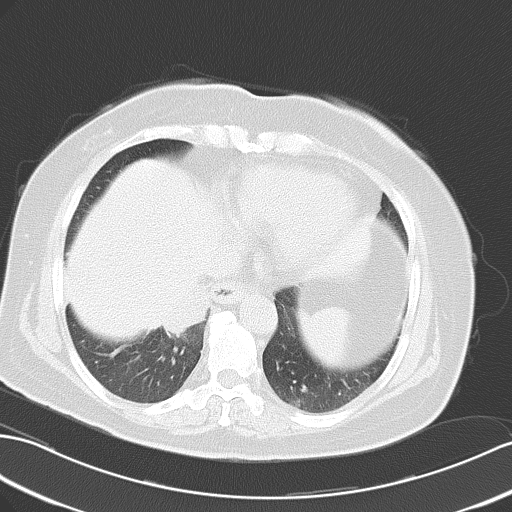
Chest CT, one axial slice. Position 16 of 50 along the scan axis. Reconstruction kernel B70f. 120 kVp. Lung window (W 1500 / L -600 HU). 5 mm slice thickness. 512 × 512 image matrix, field of view 353 × 353 mm. Female patient, age 63 years. From the clinical record (not read from this slice): clinical TNM (as recorded): T3 N0 M0.
Annotated regions visible in this slice (bounding box drawn by a radiologist):
- lung tumour (recorded histology: adenocarcinoma): bounding box (x1, y1, x2, y2) in pixels: (162, 282, 208, 339)